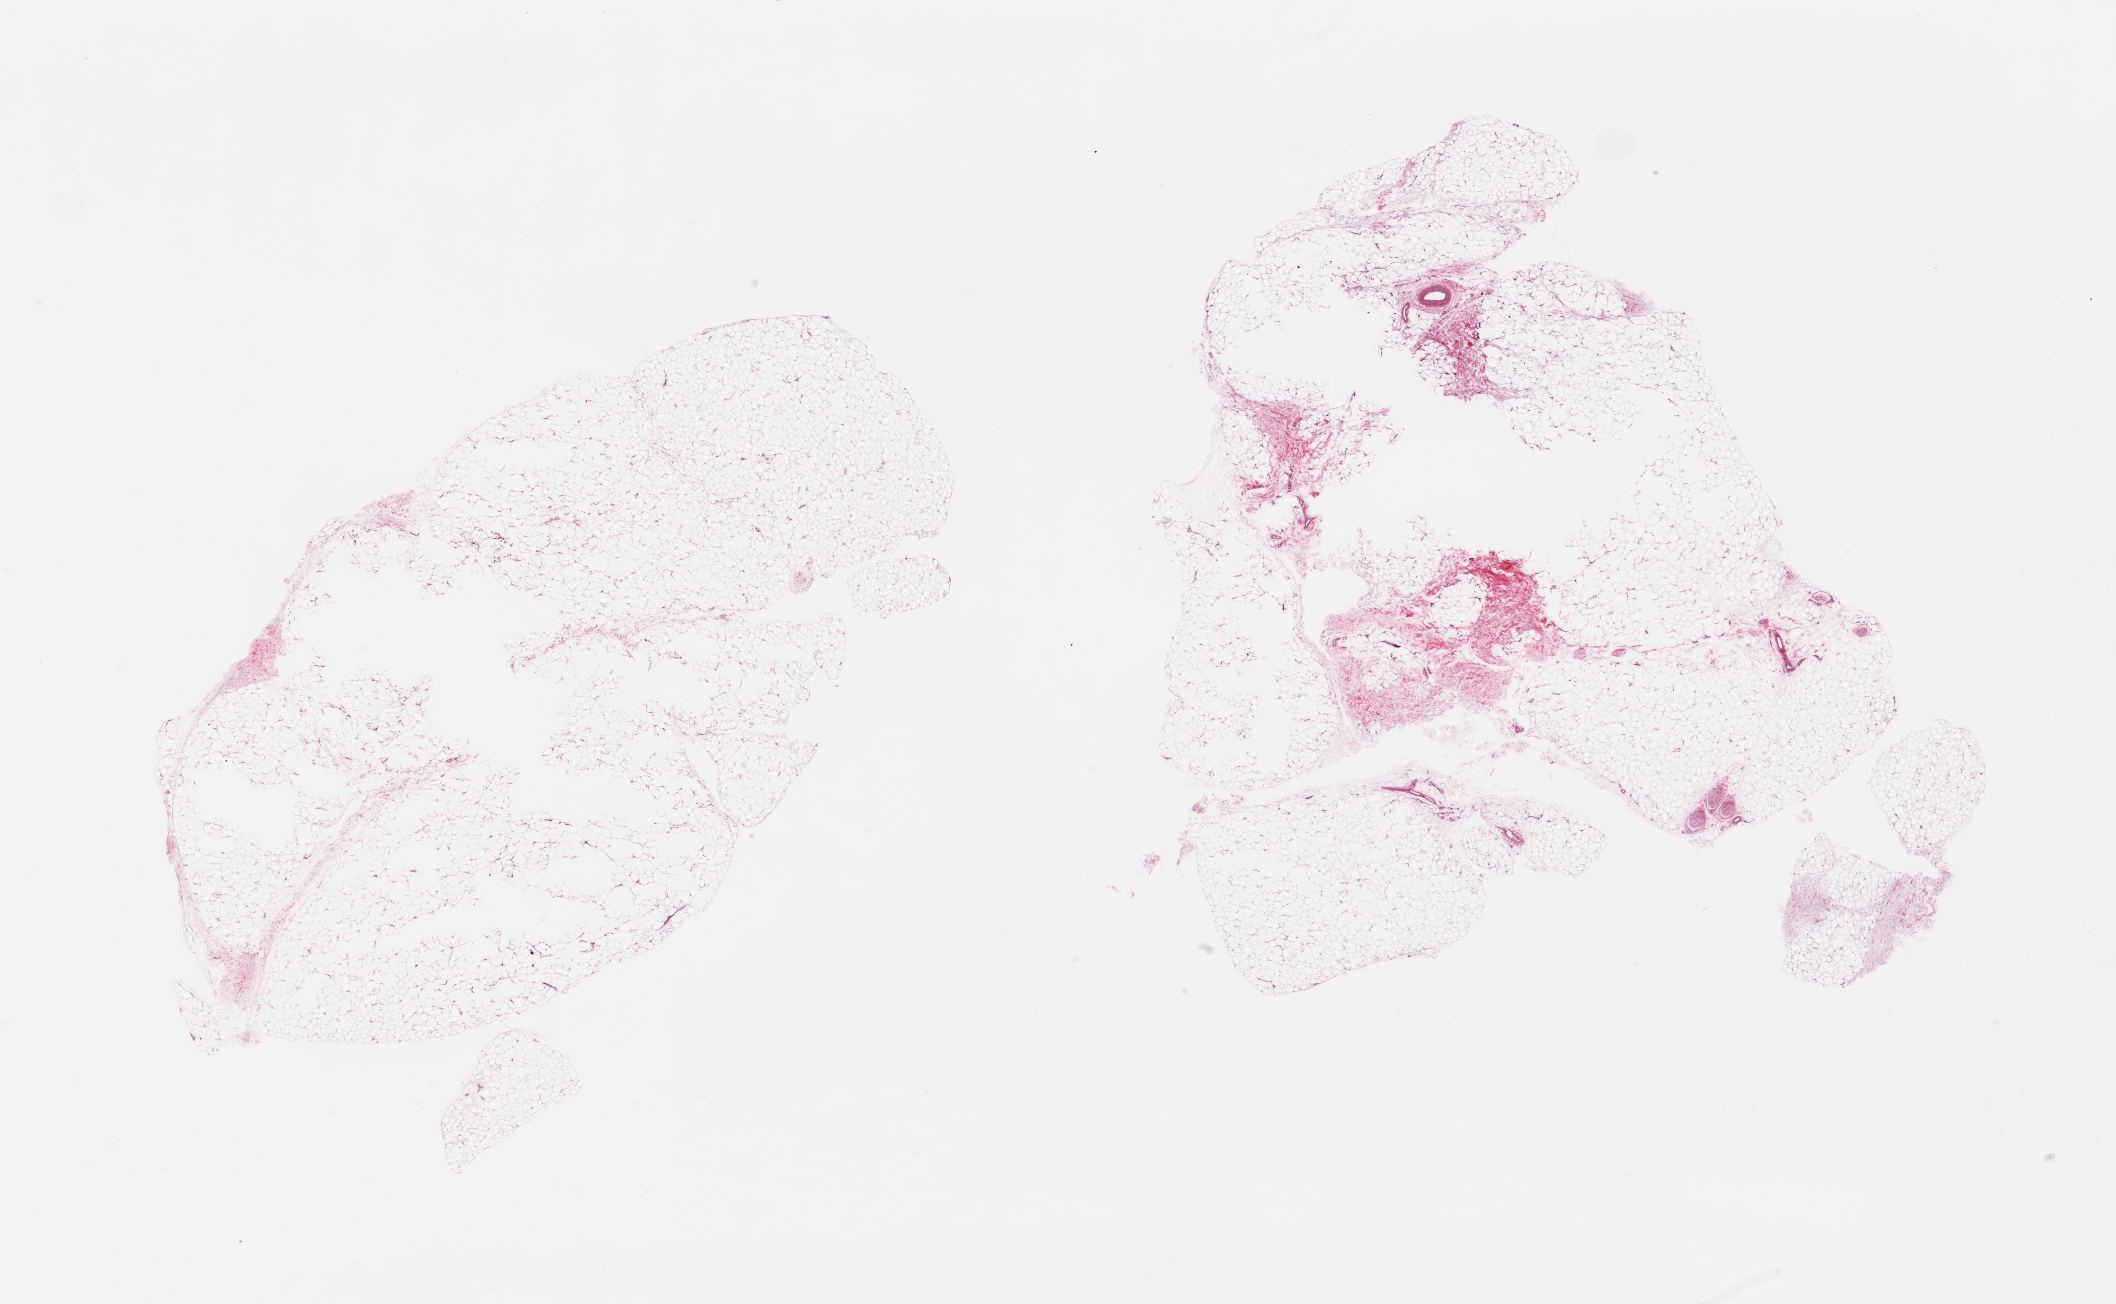
Whole-slide image, haematoxylin and eosin stain, brightfield, a low-resolution overview of the entire scanned area, about 33.5 x 20.6 mm (slide scanned at 20x), PAXgene-fixed paraffin-embedded (PFPE) section, target tissue: adipose tissue, tissue donor sample. Female donor.
Review note (as recorded): 2 pieces; central defects (?poor fixation), ~15% of 1 piece is fibrous/vessel/nerve.